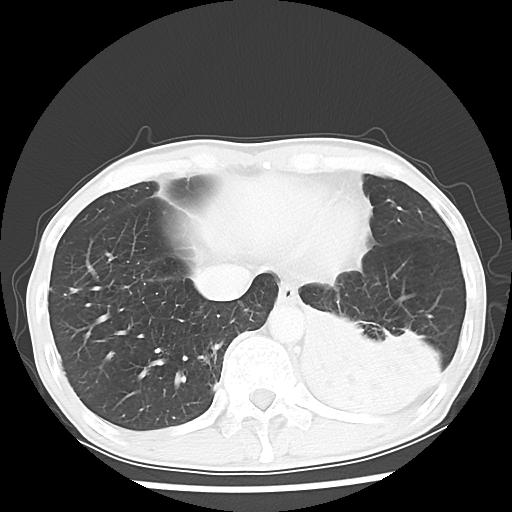
Chest CT, one axial slice. Slice 13 of 64 in the series (ordered by position). Lung window (W 1500 / L -600 HU). 5 mm slice thickness. 512 × 512 image matrix. Male patient, age 68 years. From the clinical record (not read from this slice): clinical TNM (as recorded): T4 N0 M0.
Outlined on this slice (rectangle marked by the reading radiologist):
- lung tumour (recorded histology: squamous cell carcinoma): bounding box <288,313,451,422> (left, top, right, bottom; pixels)